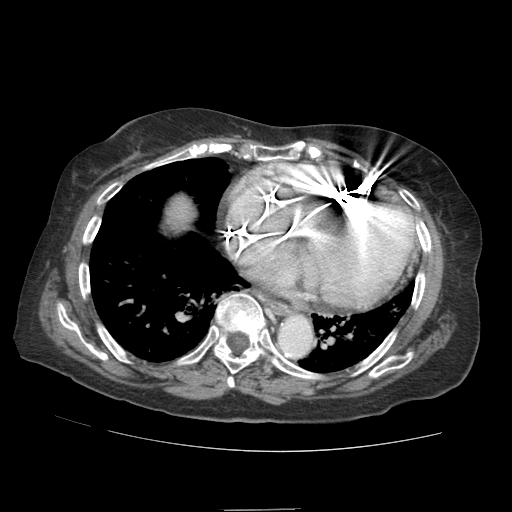
Contrast-enhanced abdominal CT (liver protocol), one axial slice. Slice 84 of 89 in the series (ordered by position). Reconstruction kernel STANDARD. Soft-tissue window (W 400 / L 40 HU). 512 × 512 image matrix, field of view 360 × 360 mm. Case-level facts recorded for this patient, not image findings: diagnosis: hepatocellular carcinoma (patient treated with transarterial chemoembolisation; whether this scan precedes or follows treatment is not stated here); TNM stage (as recorded): Stage-II; Child-Pugh class: A.
Structures marked on this image (semi-automatic segmentation, software-assisted and operator-edited):
- liver parenchyma outside the tumour (the mass and vessels are separate outlines, so this box may not span the whole liver): bounding box [x1, y1, x2, y2] px = [166, 194, 194, 230]